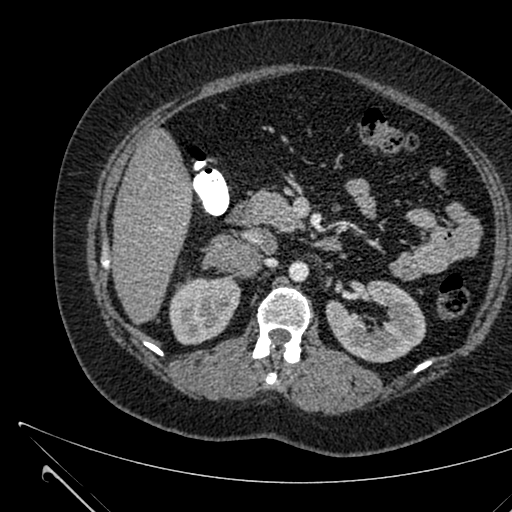
Contrast-enhanced abdominal CT, one axial slice; 120 kVp; intravenous contrast given; soft-tissue window (W 400 / L 40 HU); 1 mm slice thickness; 512 × 512 image matrix, field of view 376 × 376 mm. Female patient, age 36 years. From the clinical record (not read from this slice): diagnosis: adrenocortical carcinoma; tumour side: right adrenal; tumour size at pathology: 10 cm.
Annotated regions visible in this slice (semi-automatic segmentation, software-assisted and operator-edited):
- mass: bounding box (x1, y1, x2, y2) in pixels: (210, 234, 258, 275)